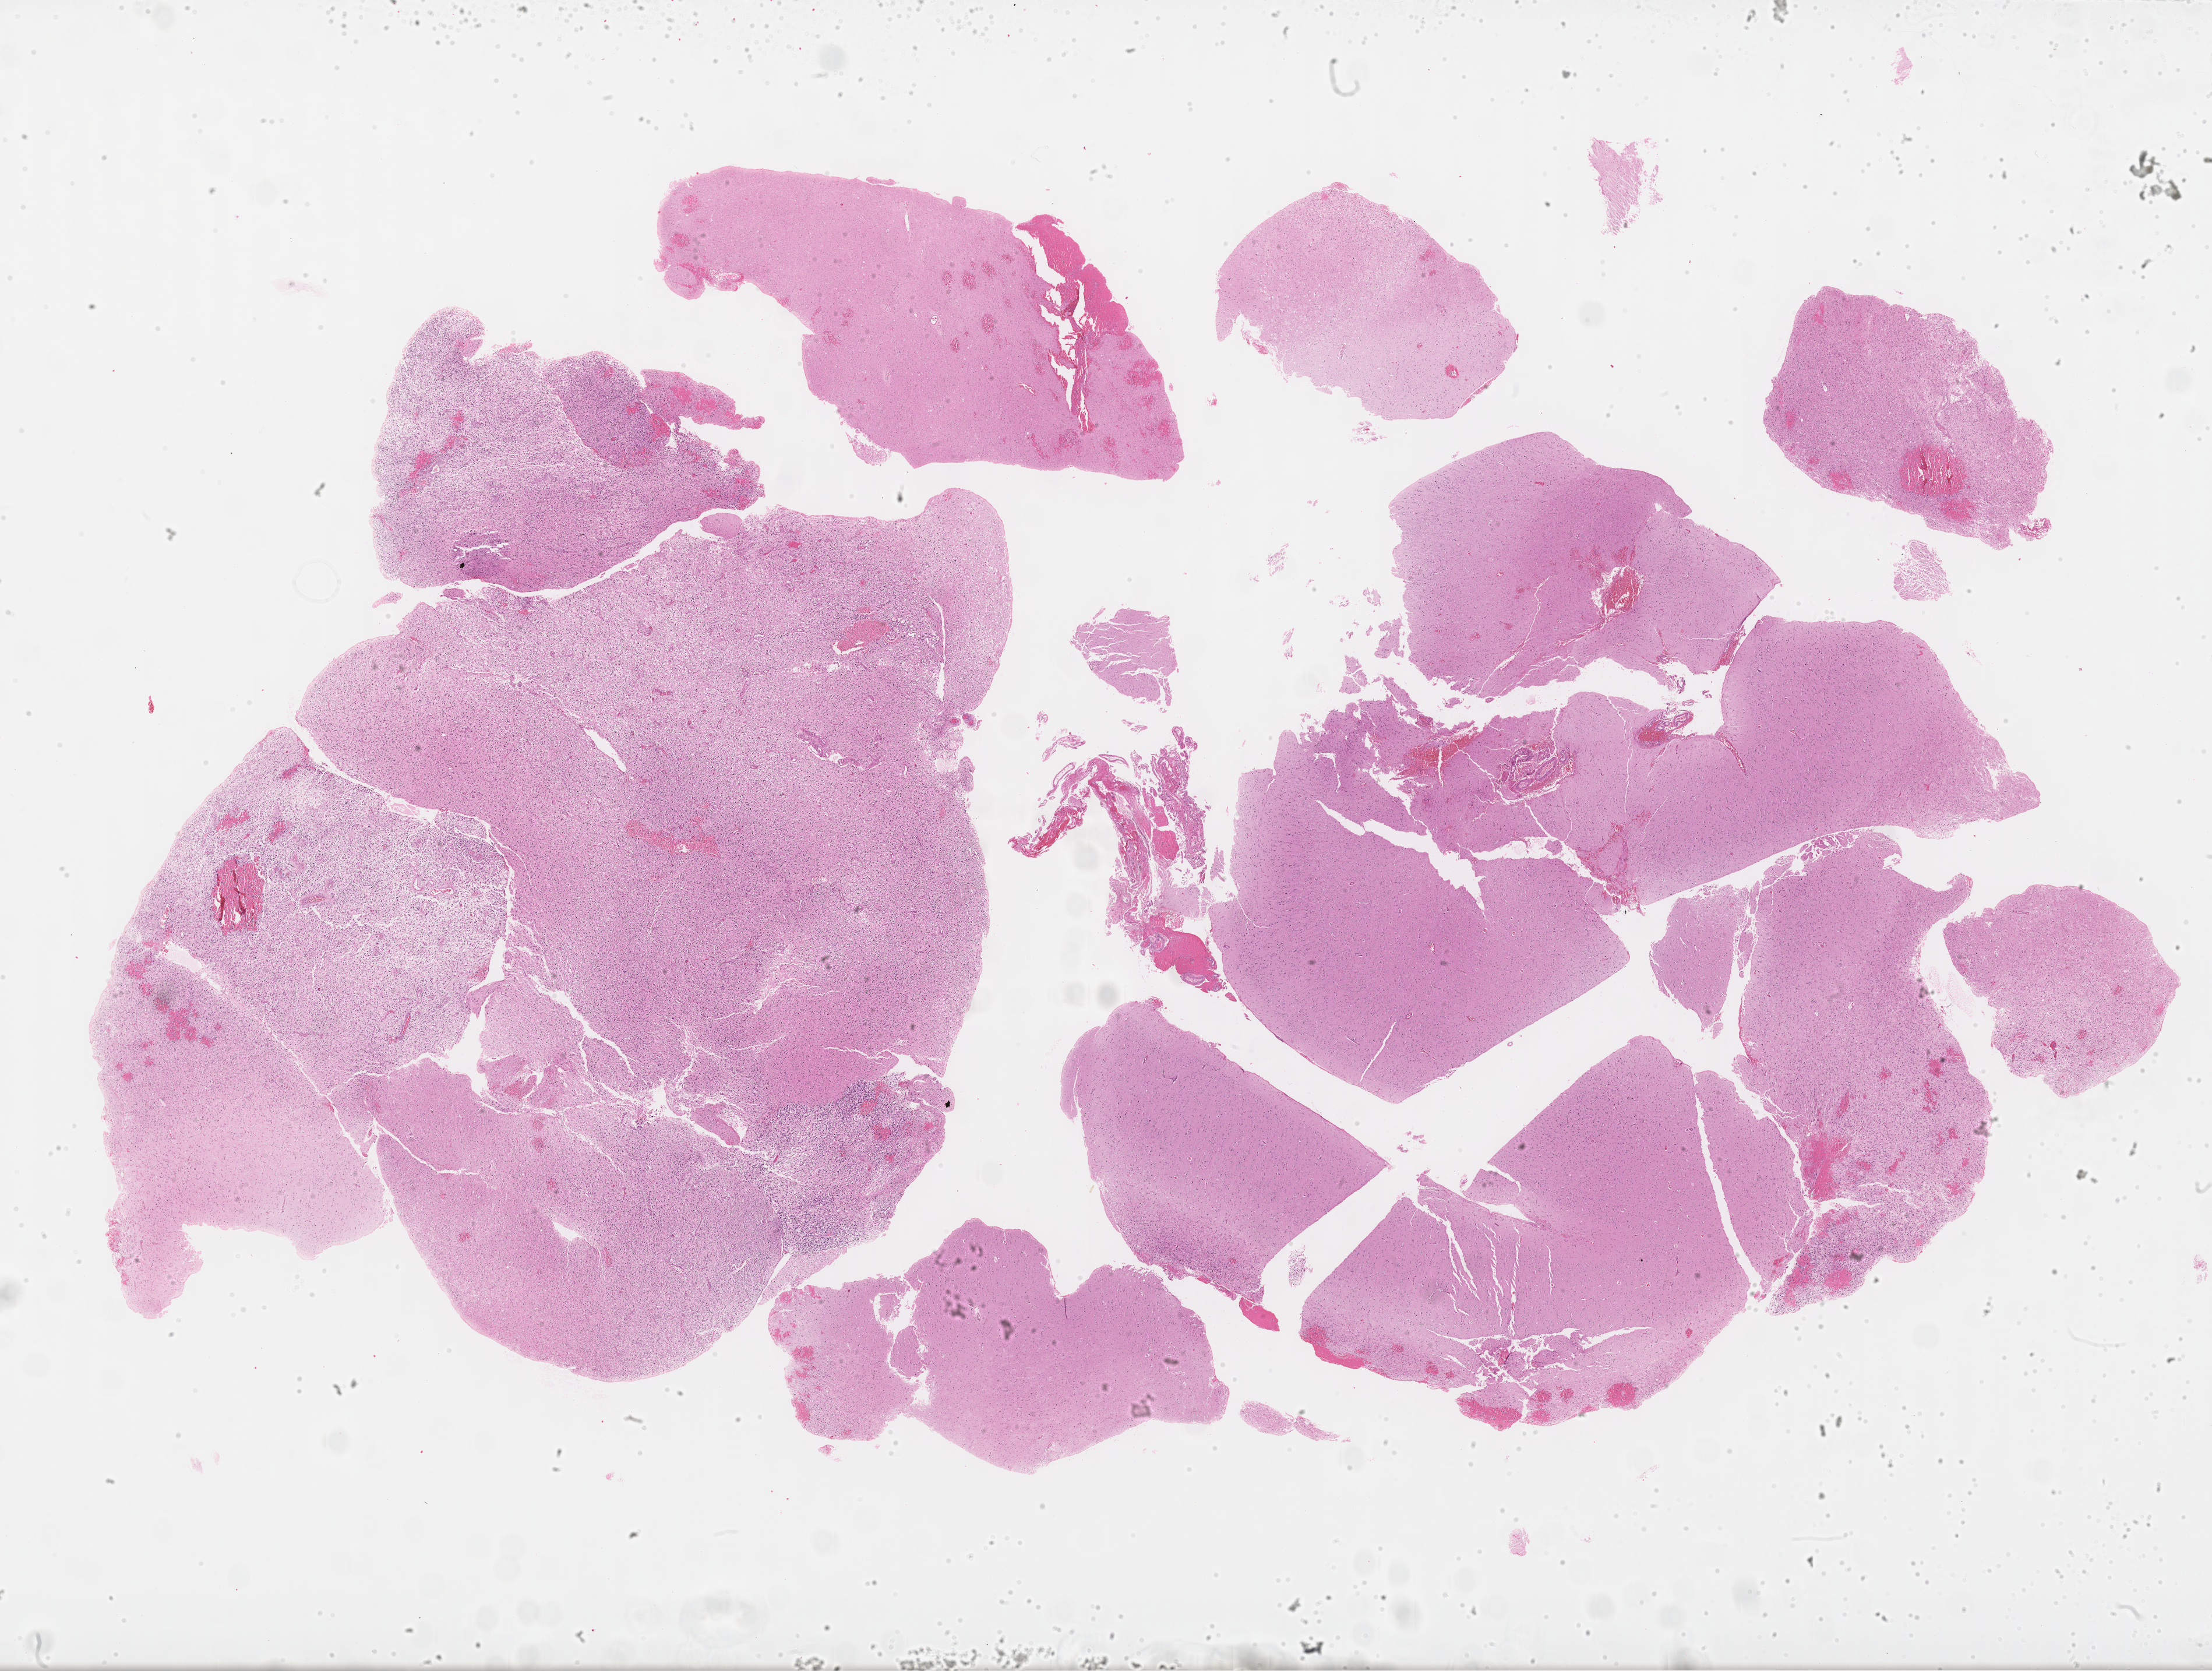
H&E-stained whole-slide image, shown as a low-resolution overview of the whole scanned area (about 30.8 x 23.2 mm). Formalin-fixed paraffin-embedded (FFPE) diagnostic section. Primary tumour sample from the brain. Female, age 68 years at initial diagnosis.
* diagnosis: Glioblastoma